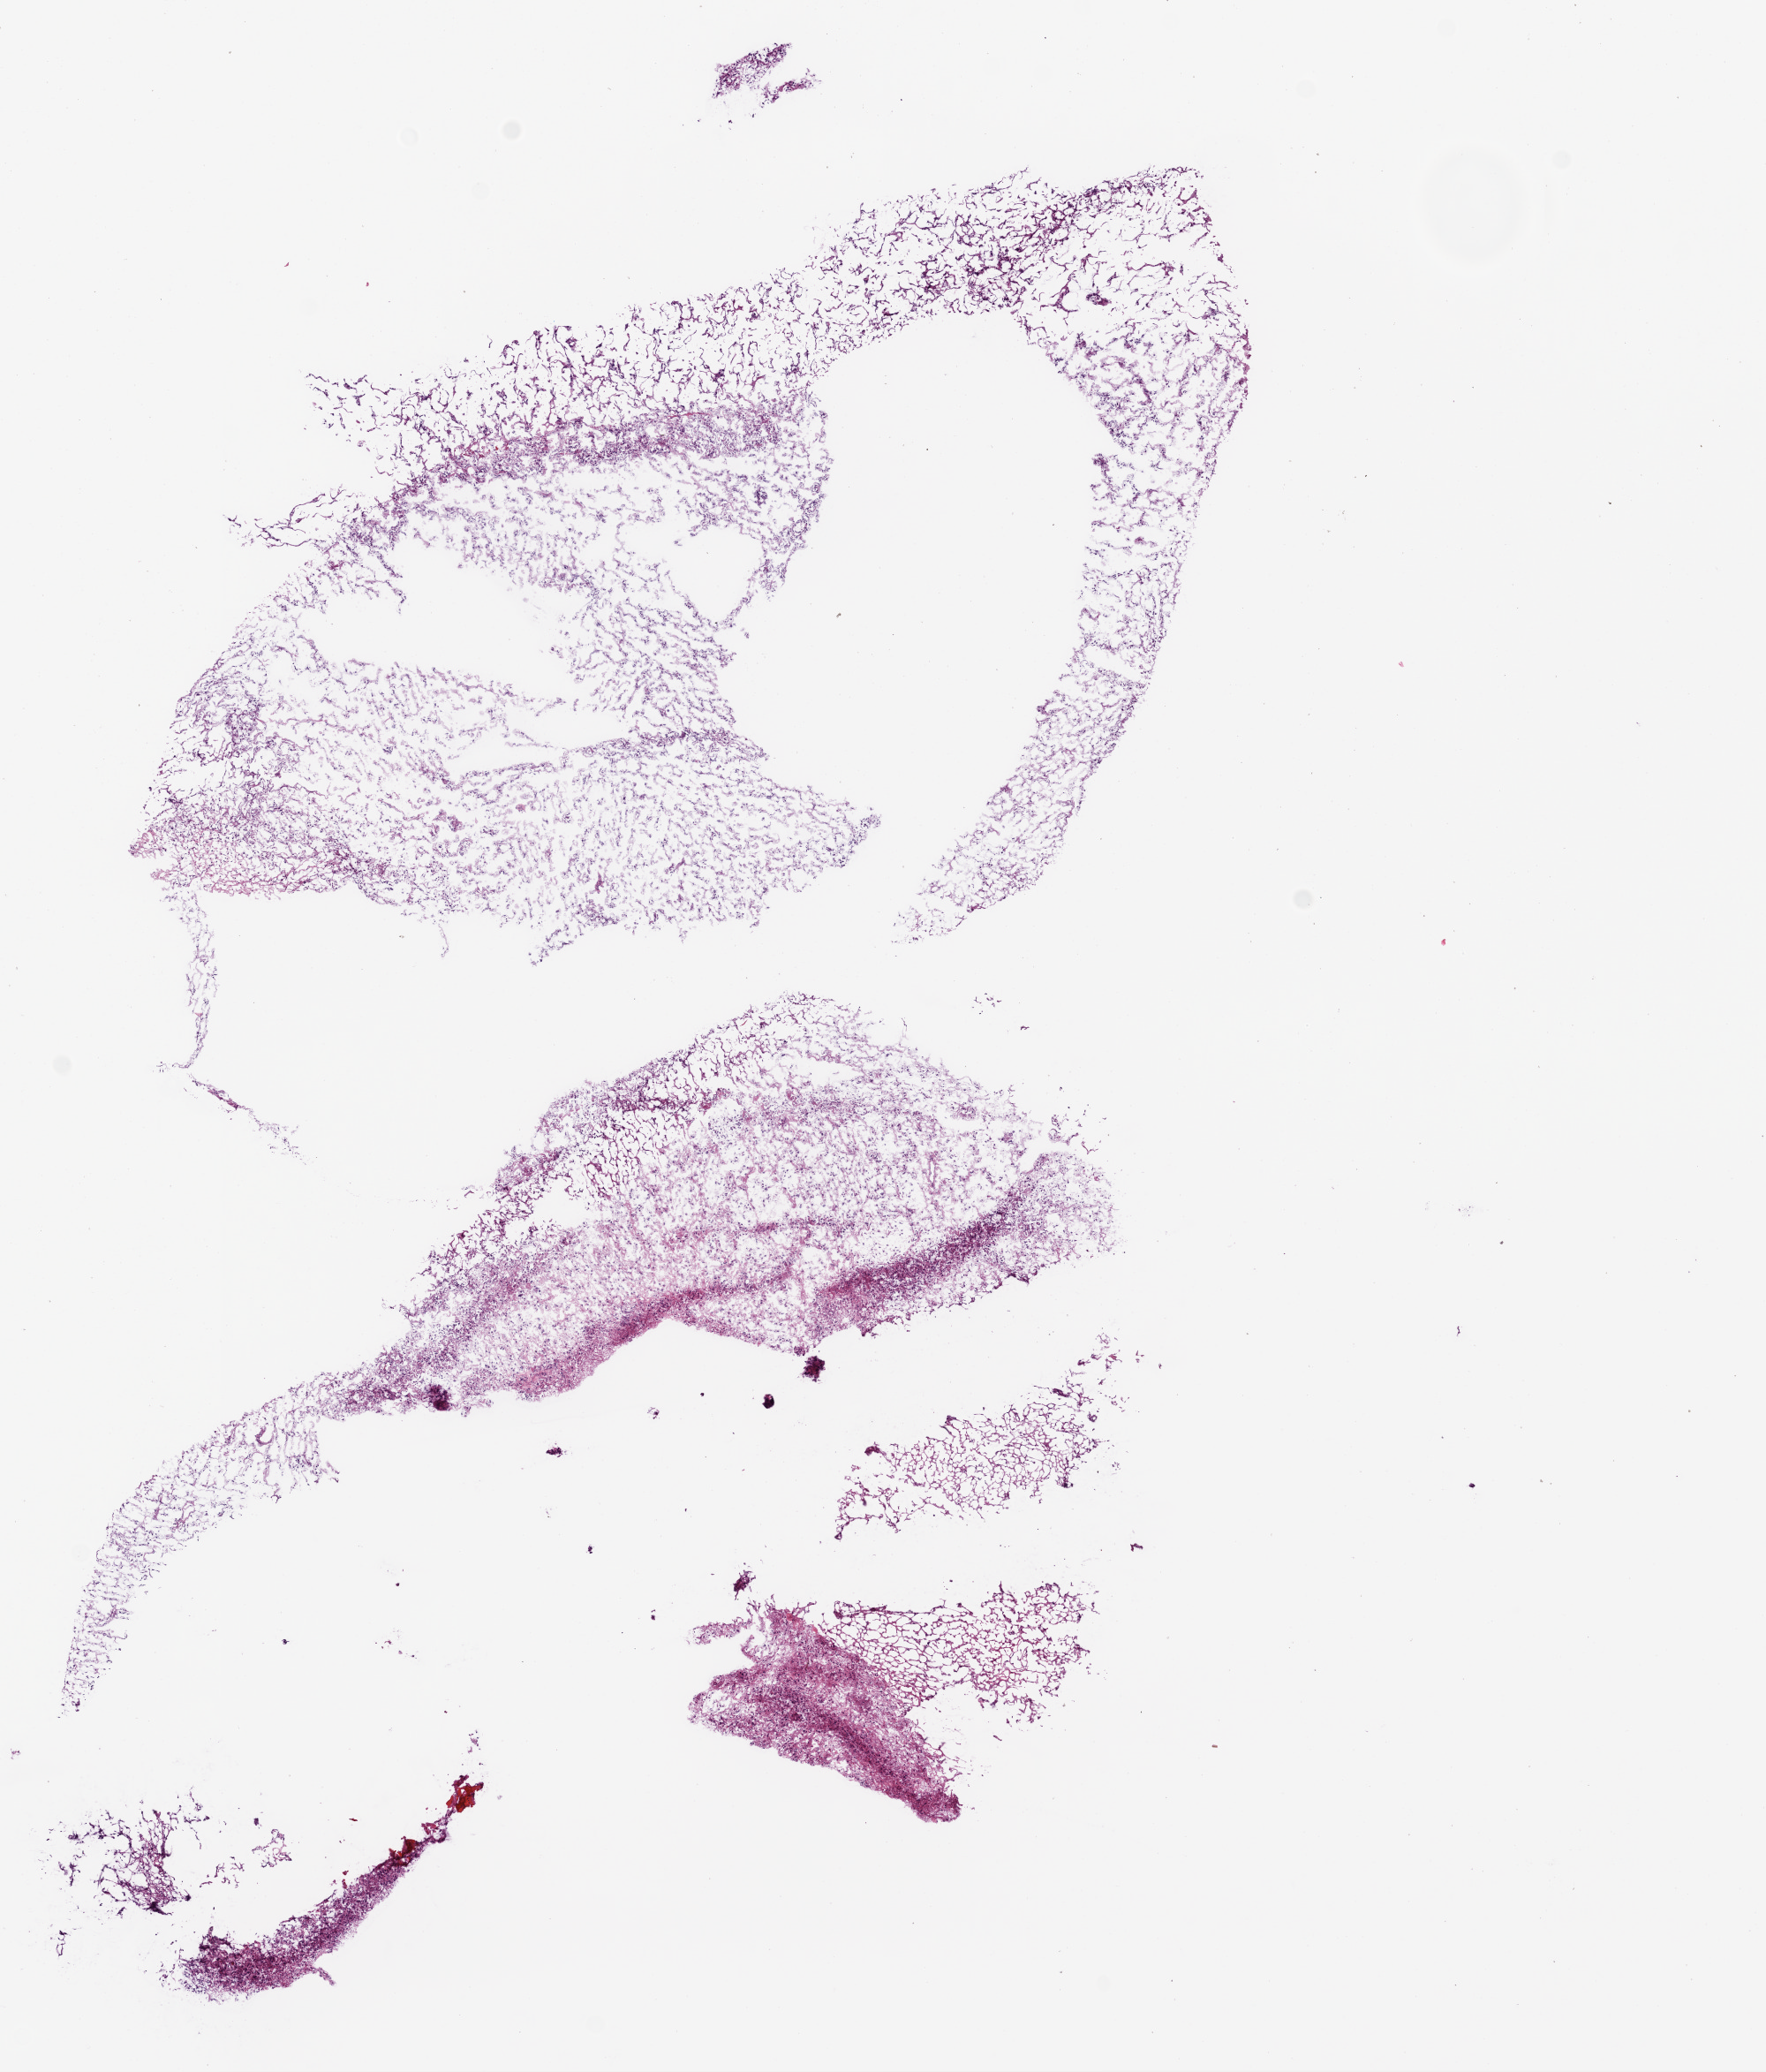
Digitized H&E-stained tissue section (whole slide), low-resolution overview of the scanned area, about 8.0 x 9.4 mm (slide scanned at 20x), frozen section from the bottom of the tissue portion, sample: primary tumour, brain. Male patient; age at initial diagnosis 23 years. Composition of this section per pathologist review: tumour cells 85%, tumour nuclei 80%.
Pathologic diagnosis: Glioblastoma.